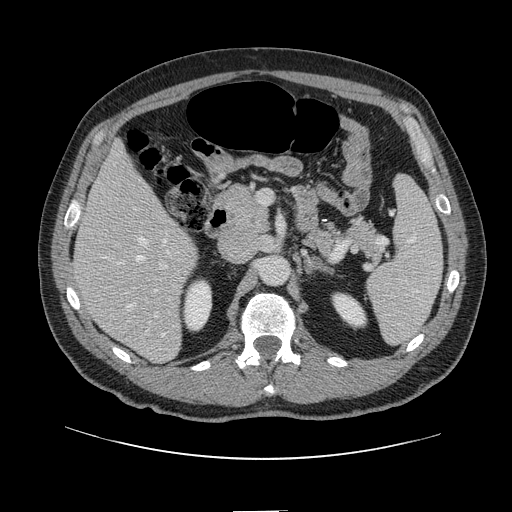
Contrast-enhanced abdominal CT, one axial slice. Soft-tissue window (W 400 / L 40 HU). 2.5 mm slice thickness. 512 × 512 image matrix, field of view 412 × 412 mm. Male patient, age 66 years. From the clinical record (not read from this slice): diagnosis: colorectal cancer liver metastases, imaged before liver resection; multiple liver metastases: no; largest metastasis: 3.5 cm; disease in both lobes: no.
Annotated regions visible in this slice (manually delineated by an expert):
- hepatic veins: box from (x=127, y=237) to (x=169, y=336) px
- liver: (x=74, y=144)–(x=198, y=362)
- planned liver remnant (the part of the liver to remain after resection): (x=74, y=144)–(x=175, y=285)
- portal vein (with intrahepatic branches): (x=153, y=261)–(x=168, y=314)